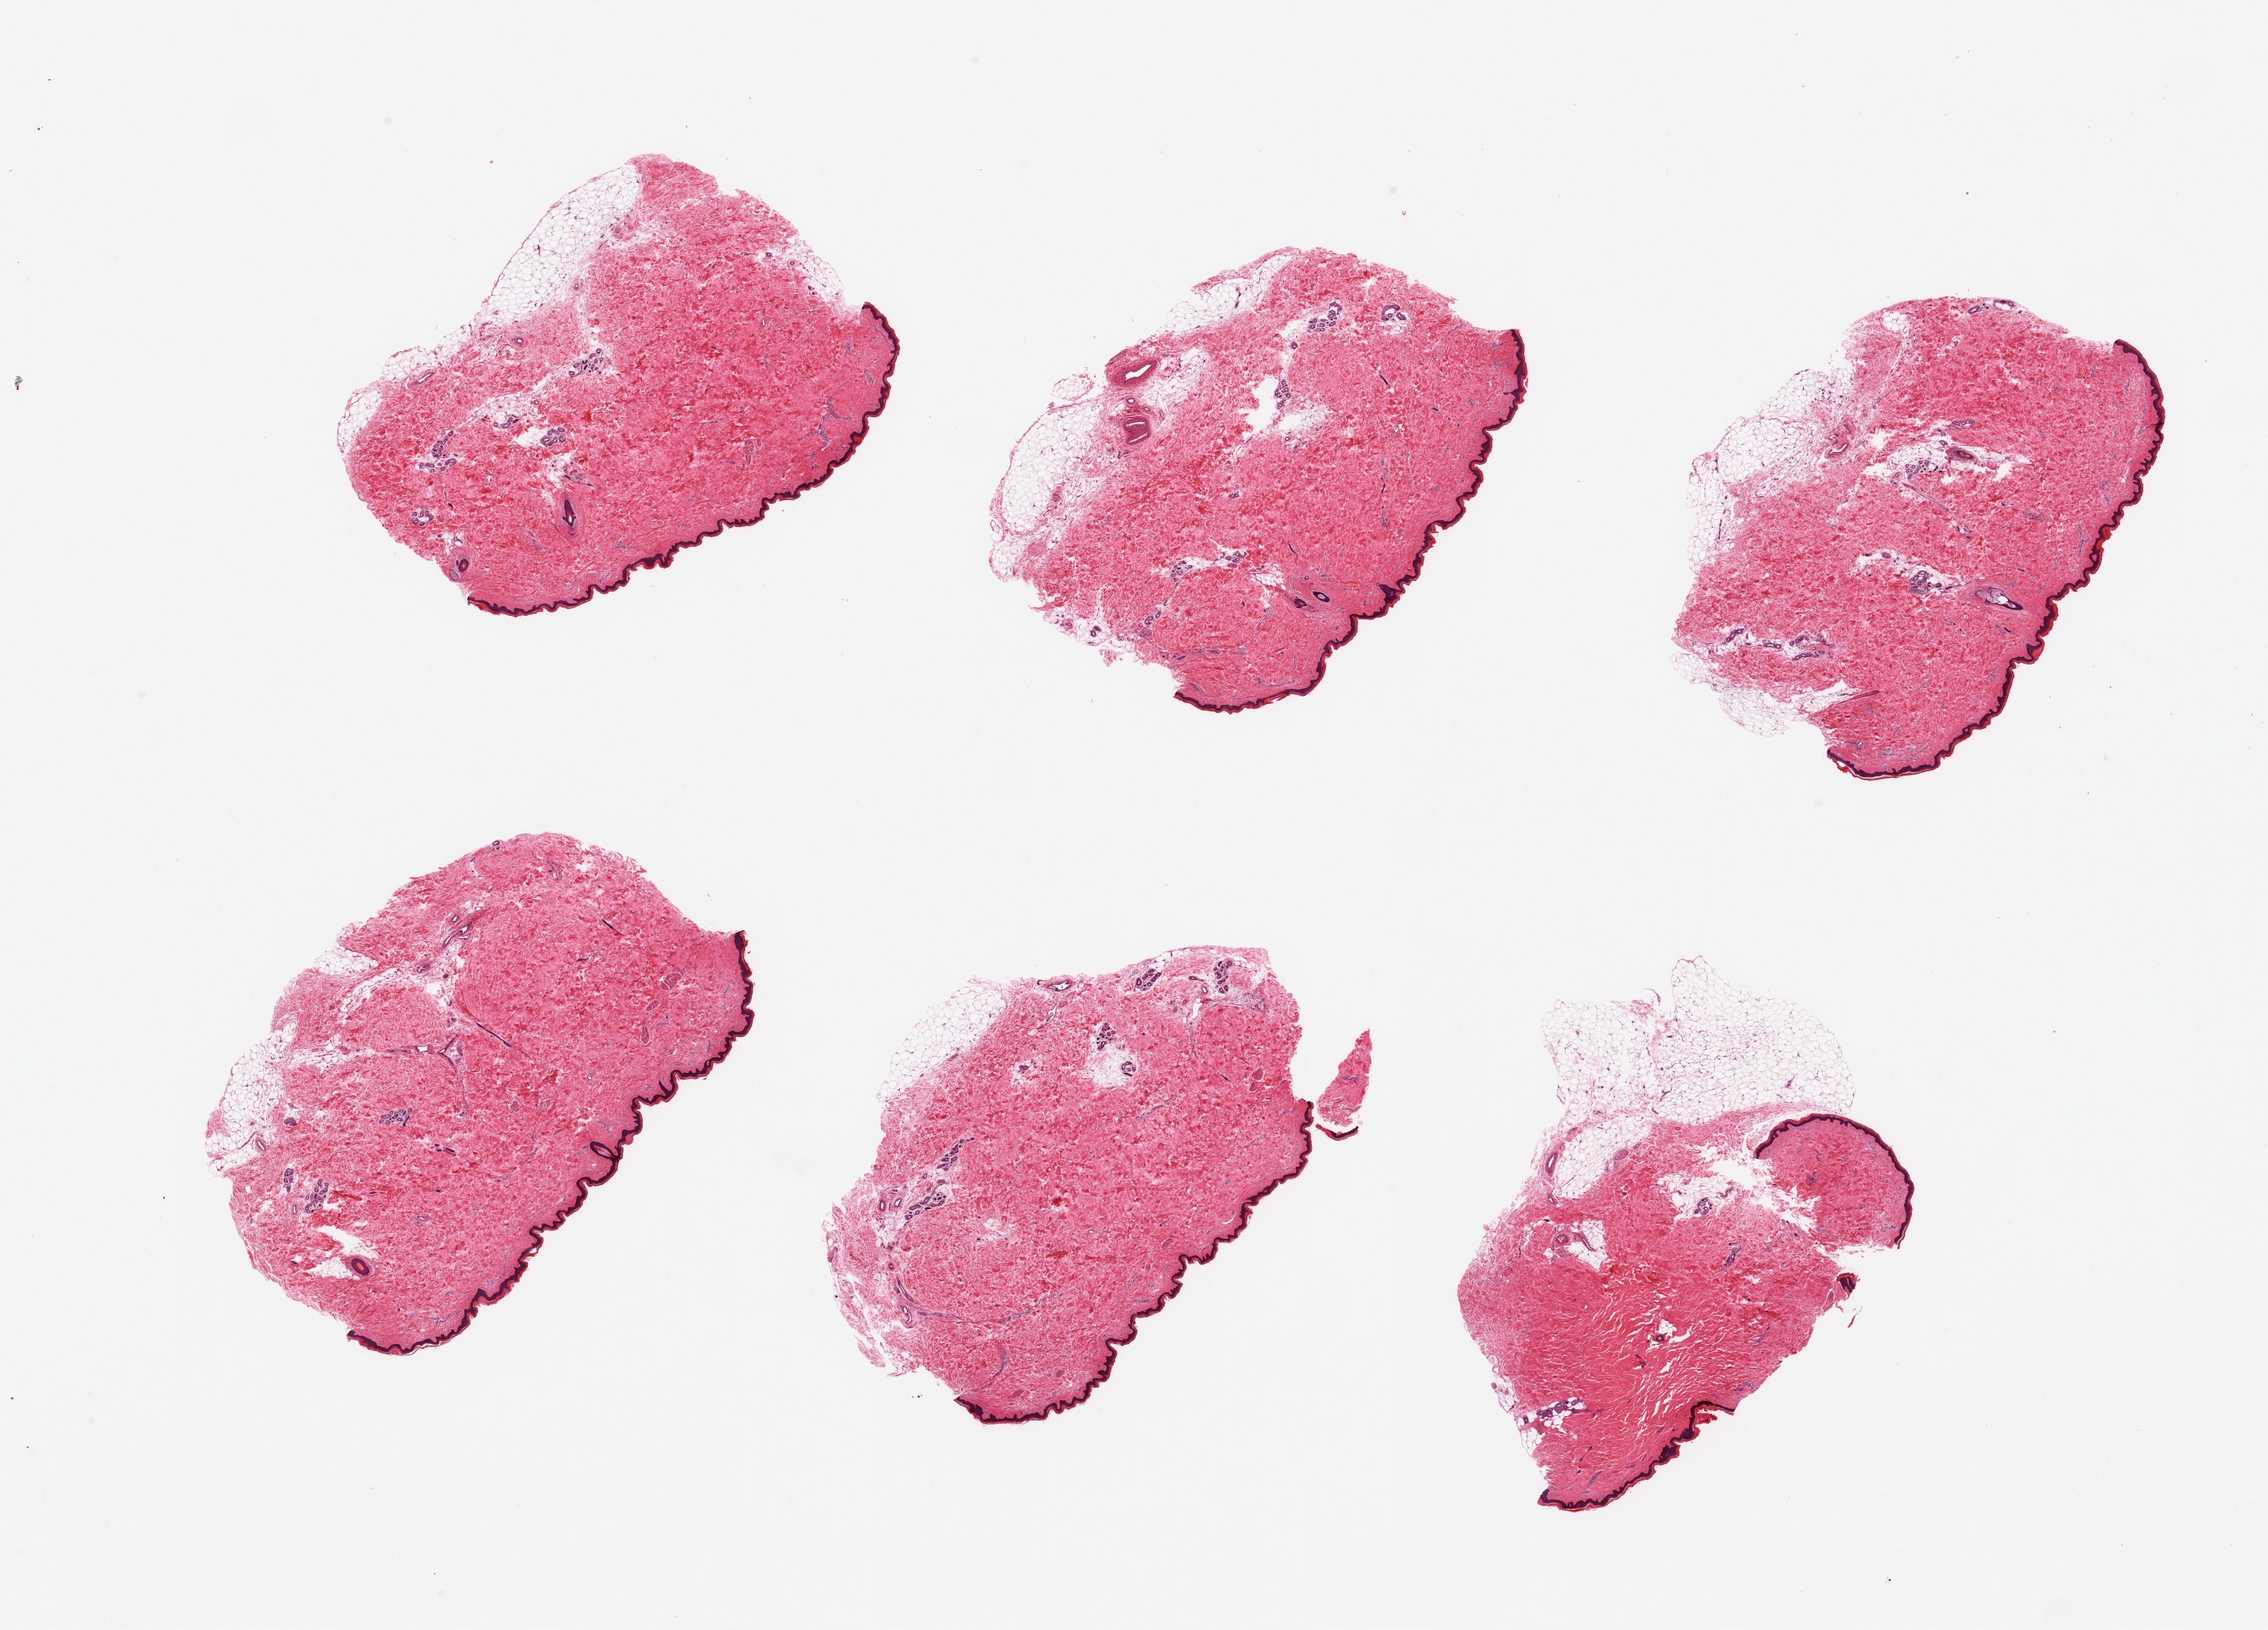
H&E whole-slide image, low-resolution overview of the scanned area, about 25.6 x 18.4 mm (acquisition: 20x scan). PAXgene-fixed paraffin-embedded (PFPE) section. Section of skin of lower leg (target tissue). Donor tissue sample. Donor: female.
Reviewer comment on this tissue sample: 6 pieces; 10% to 30% external fat; insignificant periadnexal fat; ~37 microns thick epidermis.